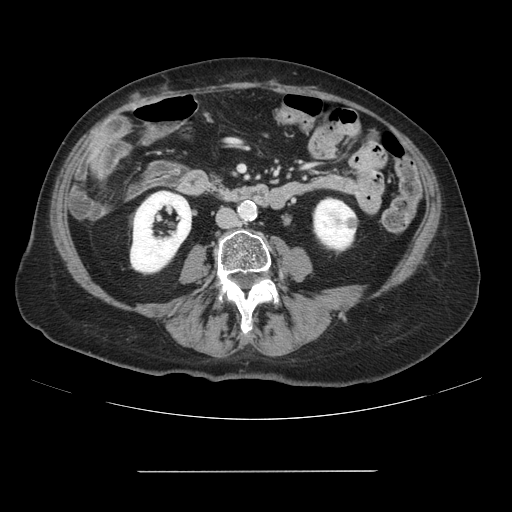
Contrast-enhanced abdominal CT, one axial slice; slice 5 of 111 in the series (ordered by position); intravenous contrast given; soft-tissue window (W 400 / L 40 HU); 512 × 512 image matrix, field of view 400 × 400 mm. Female patient, age 74 years. Case-level facts recorded for this patient, not image findings: diagnosis: colorectal cancer liver metastases, imaged before liver resection; multiple liver metastases: yes; largest metastasis: 1.1 cm; disease in both lobes: yes.
Annotated regions visible in this slice (expert manual segmentation):
- liver: bounding box <93,134,107,160> (left, top, right, bottom; pixels)